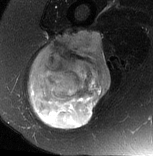
MRI of an extremity soft-tissue mass, one axial slice; position 40 of 77 along the scan axis; T2-weighted fat-saturated; MR volume resampled by the dataset authors to the PET/CT grid (not the native acquisition matrix); 3.27 mm slice thickness; 153 × 156 image matrix. Female patient. Case-level facts recorded for this patient, not image findings: histological type: synovial sarcoma; grade: intermediate; site of the primary tumour: right buttock.
Annotated regions visible in this slice (expert contour drawn on MRI and transferred to this co-registered scan by the dataset authors):
- gross tumour volume including surrounding oedema: box from (x=28, y=29) to (x=111, y=130) px
- gross tumour volume (mass): (x=28, y=29)–(x=111, y=130)